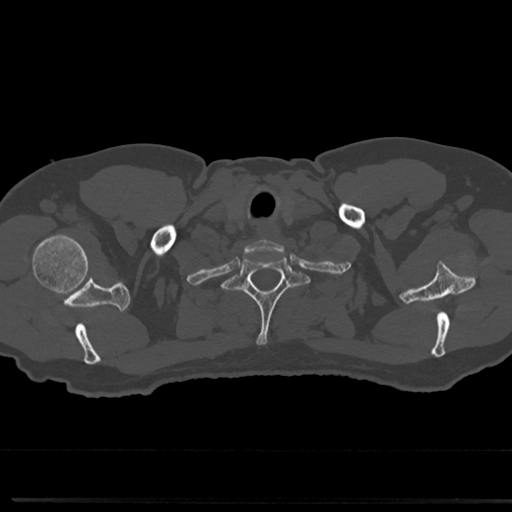
CT including the spine, one axial slice. Slice 676 of 817 in the series (ordered by position). Reconstruction kernel Br40s/3. 120 kVp. Bone window (W 1800 / L 400 HU). 0.5 mm slice thickness. 512 × 512 image matrix, field of view 355 × 355 mm. Patient: male, 61 years. Case-level facts recorded for this patient, not image findings: primary cancer: prostate.
Outlined on this slice (semi-automatic segmentation, software-assisted and operator-edited):
- T1 vertebra: bounding box [x1, y1, x2, y2] px = [229, 251, 304, 347]
- T2 vertebra: [212, 292, 315, 313]